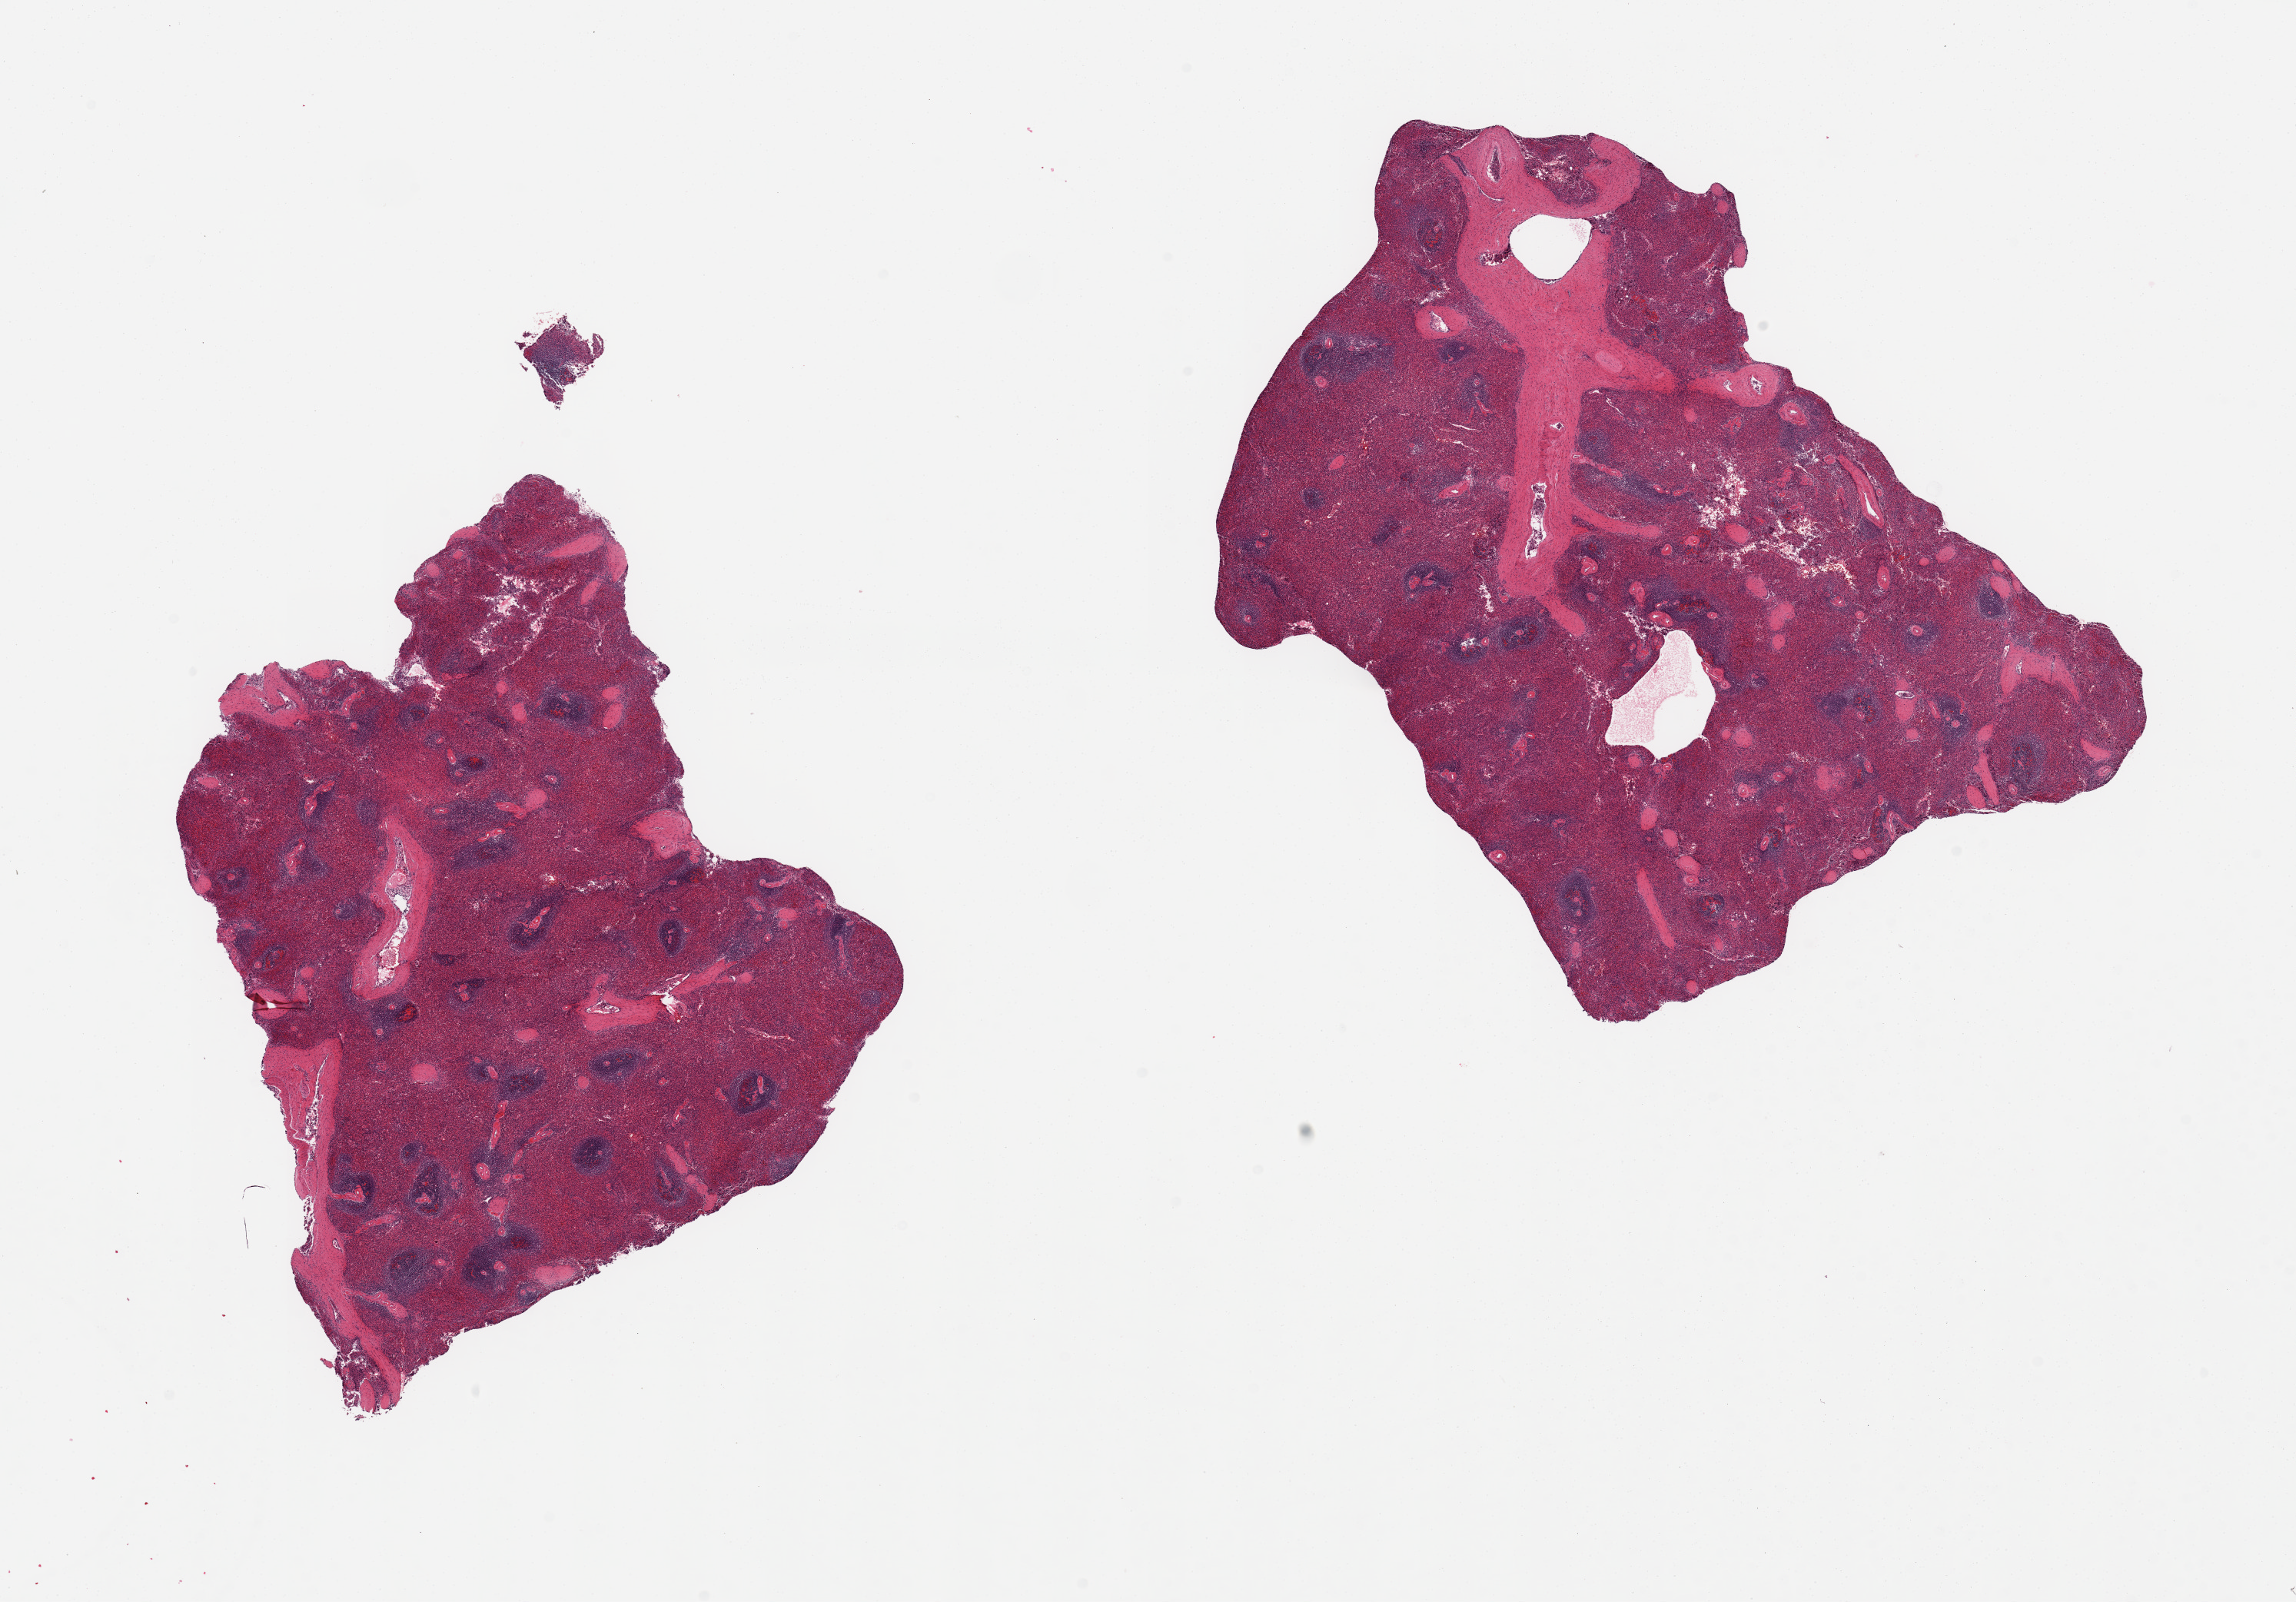
H&E whole-slide image, whole scanned area (about 23.6 x 16.5 mm, slide scanned at 20x) shown as a low-resolution overview. PAXgene-fixed, paraffin-embedded tissue. Section of spleen (target tissue). Tissue donor sample. Donor sex: male.
Review note (as recorded): 2 pieces.